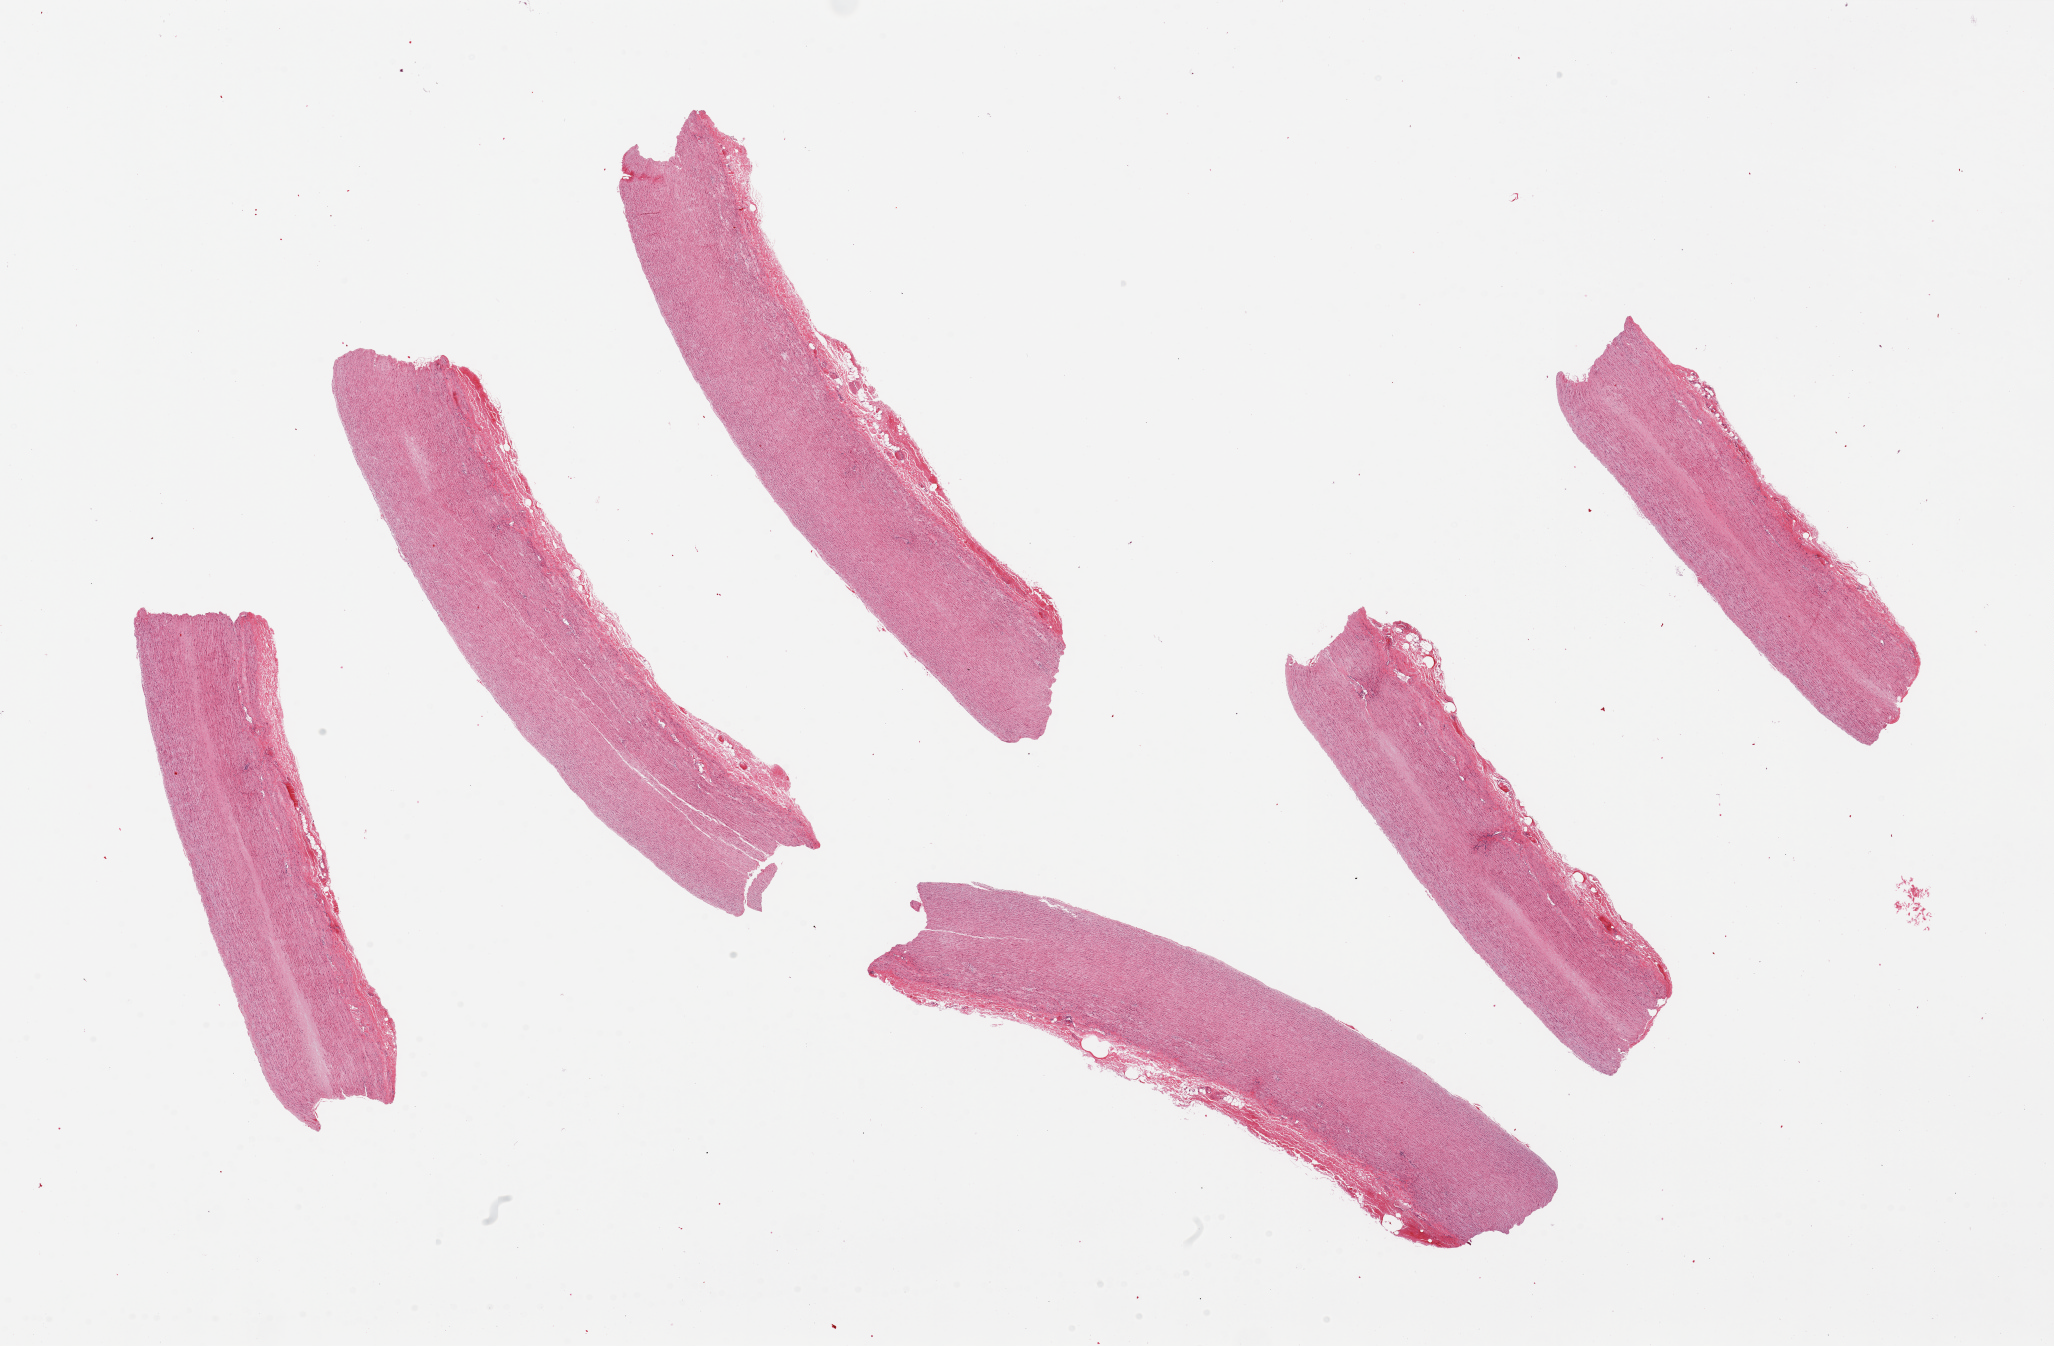
Digitized H&E-stained section — whole scanned area (about 32.5 x 21.3 mm, slide scanned at 20x) shown as a low-resolution overview; PAXgene-fixed, paraffin-embedded tissue; target tissue: aorta; donor tissue sample. Donor: male.
Reviewer comment on this tissue sample: 6 pieces. well trimmed. no plaques.